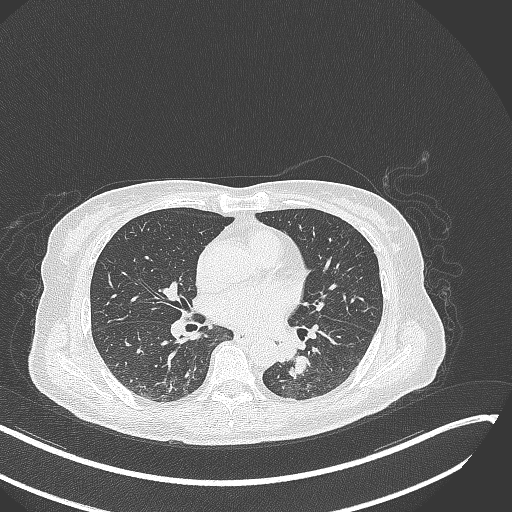
Chest CT, one axial slice. Slice 129 of 342 in the series (ordered by position). 120 kVp. Lung window (W 1500 / L -600 HU). 1 mm slice thickness. 512 × 512 image matrix. Female patient, age 64 years. From the clinical record (not read from this slice): clinical TNM (as recorded): T3 N1 M1; histopathological grade: G3.
Annotated regions visible in this slice (bounding box drawn by a radiologist):
- lung tumour (recorded histology: small cell carcinoma): bounding box (x1, y1, x2, y2) in pixels: (270, 336, 316, 382)